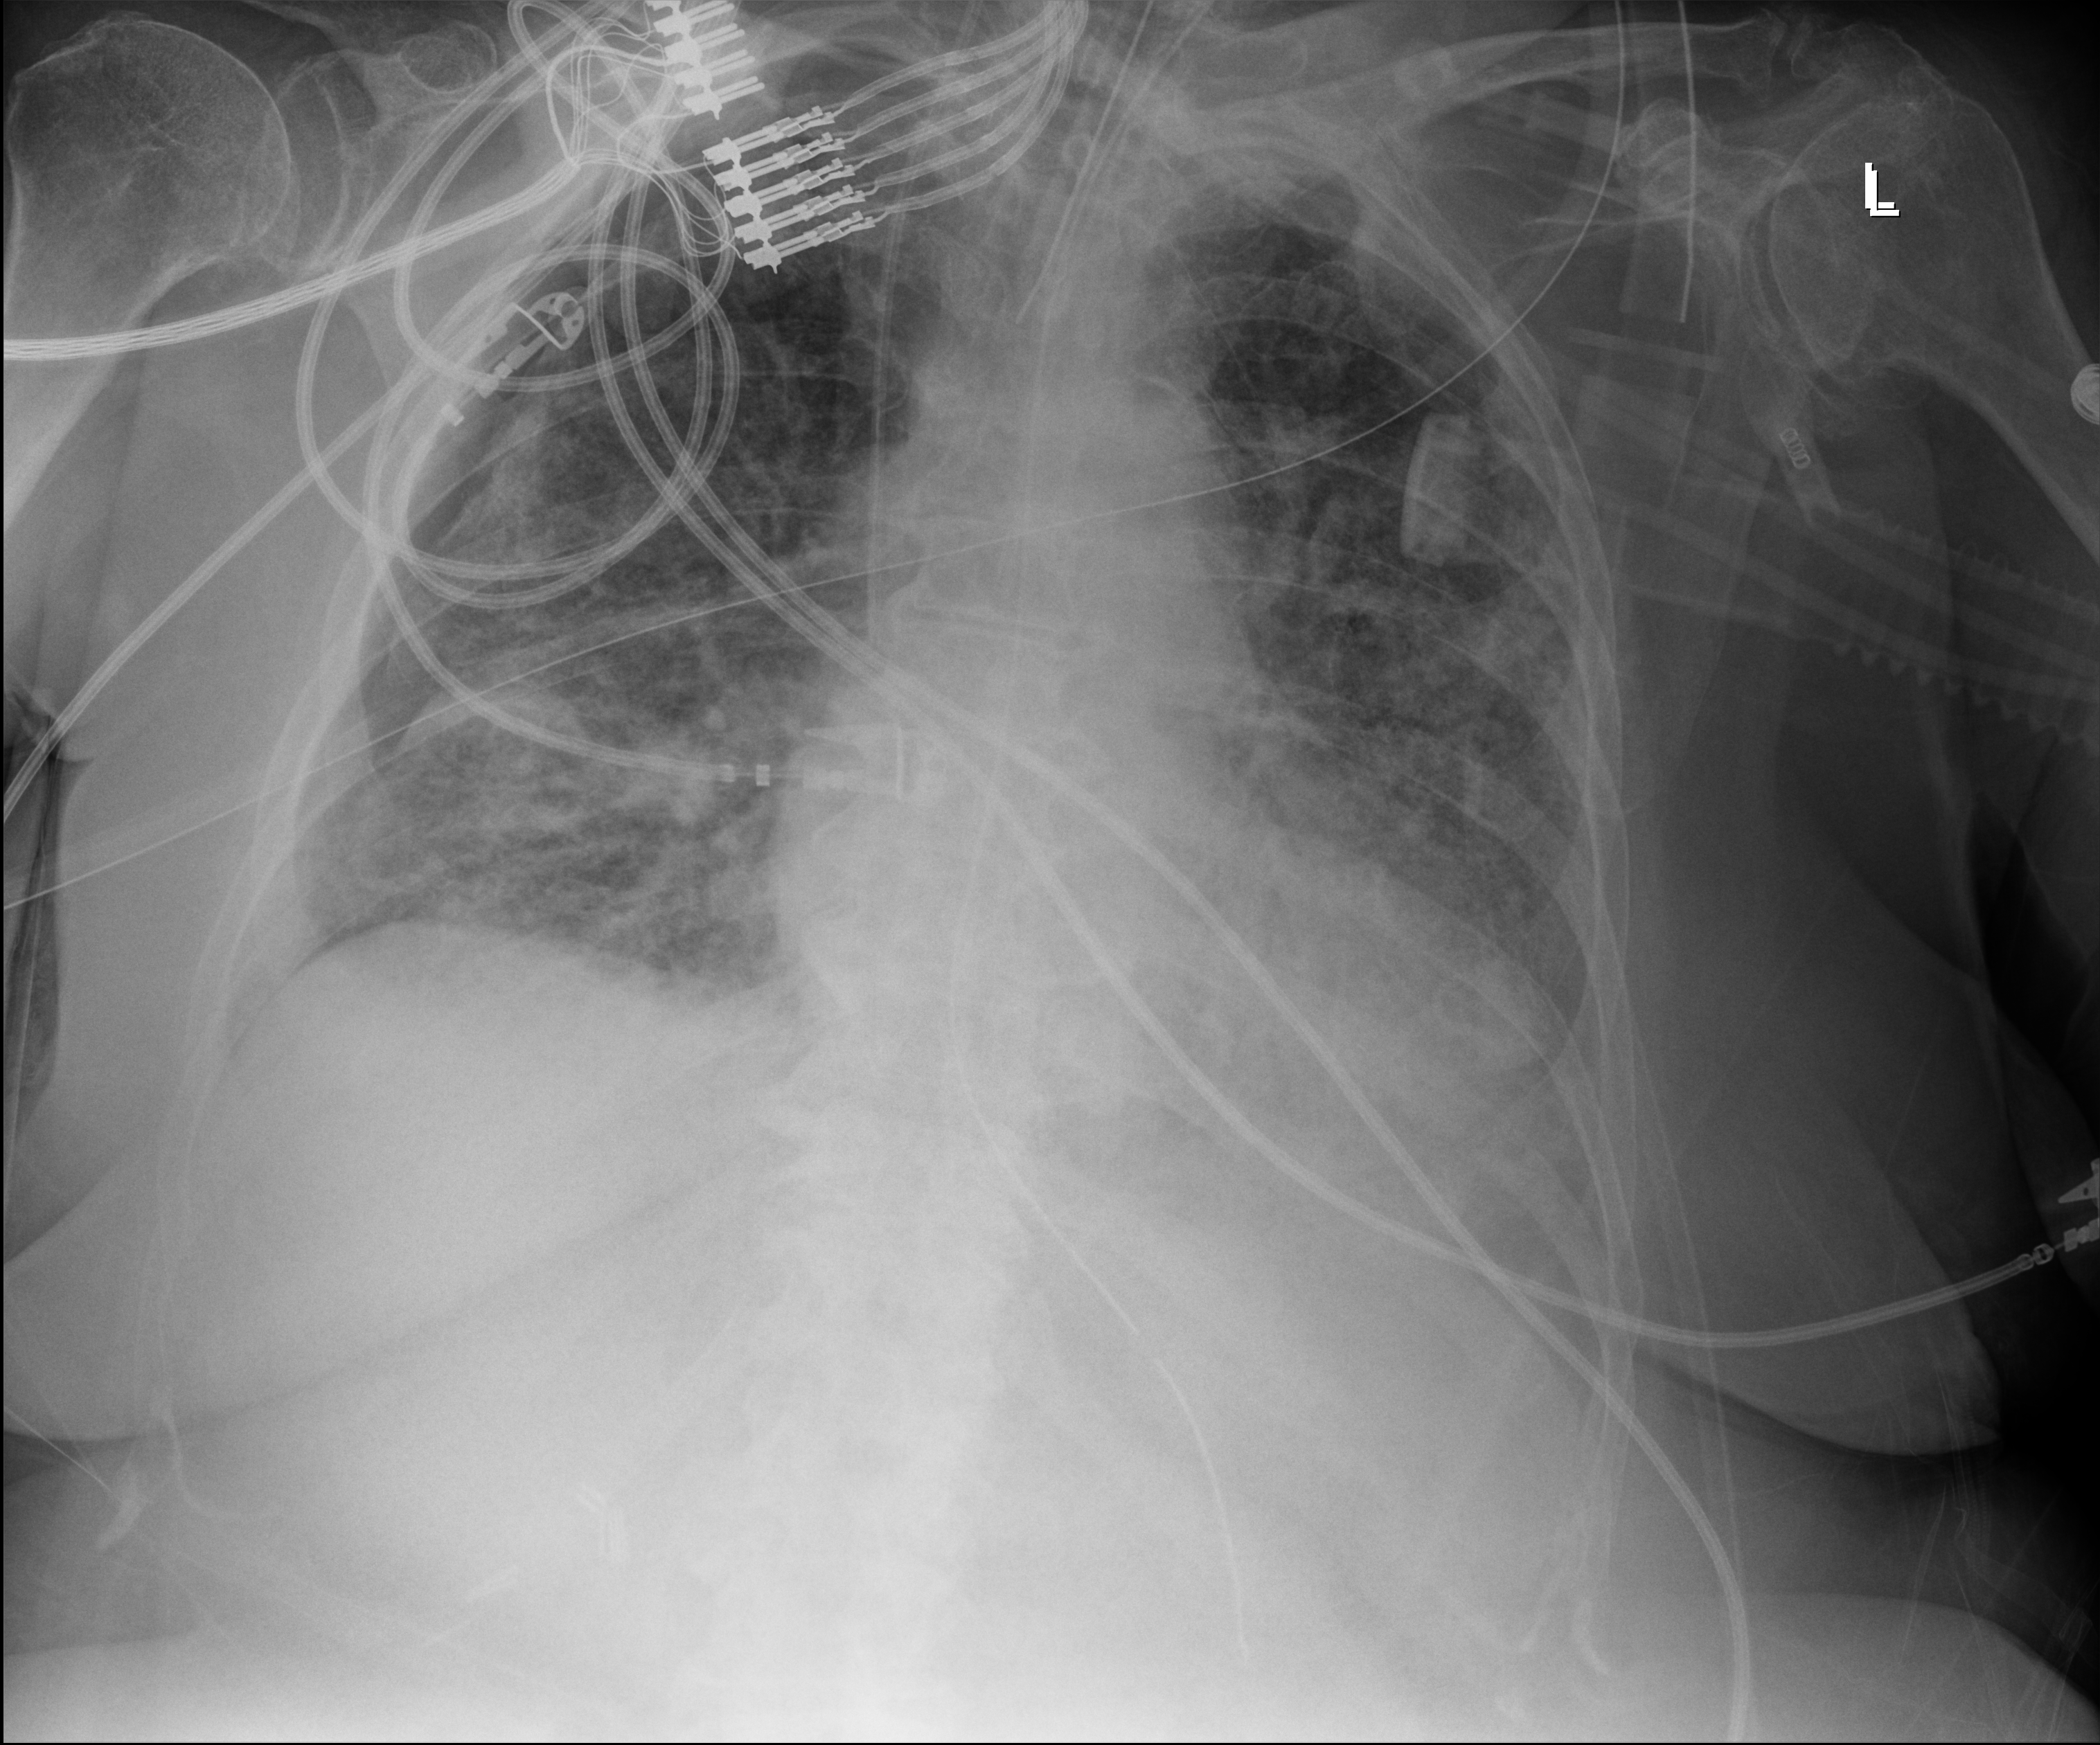
Bedside chest radiograph (digital radiography); anteroposterior (AP) projection. Female patient hospitalised with COVID-19, age 75–90 years.
Hospital-stay facts (about this admission, not read from this image; timing relative to this image not recorded): mechanically ventilated during this hospital stay: yes; chronic kidney disease (admission record): no.